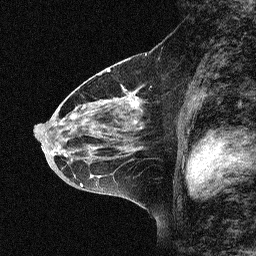
Breast MRI (dynamic contrast-enhanced), one sagittal slice; slice 34 of 64 in the series (ordered by position); dynamic contrast-enhanced study with each time point stored as its own series, time point 2 of 3 at this slice position (early post-contrast, ordered by acquisition time); 1.5 T; TE 4.5 ms, TR 11 ms; 2.06 mm slice thickness; 256 × 256 image matrix, field of view 200 × 200 mm. Patient: female, 46 years. From the clinical record (not read from this slice): setting: breast cancer imaged before/during neoadjuvant chemotherapy; receptor status: HER2-positive.
Outlined on this slice (semi-automatic segmentation, software-assisted and operator-edited):
- analysis volume of interest (the breast-tissue region the enhancement analysis was run in; not a lesion): box from (x=46, y=51) to (x=180, y=169) px
- tumour enhancement mask (voxels above the 90 % enhancement threshold inside the analysis volume of interest): (x=123, y=91)–(x=137, y=107)